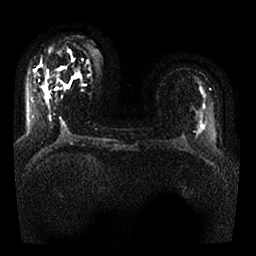
Breast MRI, one axial slice; slice 12 of 25 in the series (ordered by position); diffusion-weighted series; image 2 of 4 stored at this slice position (different b-values; order by instance number); 1.5 T; 4 mm slice thickness; 256 × 256 image matrix. Female patient.
Outlined on this slice (expert manual segmentation):
- tumour on diffusion-weighted imaging: bounding box <44,87,47,93> (left, top, right, bottom; pixels)